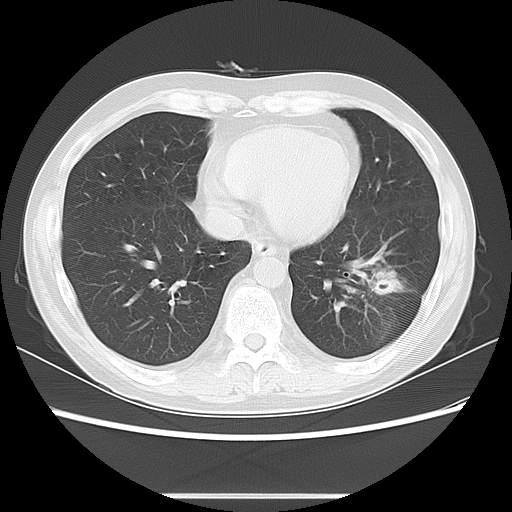
Chest CT, one axial slice. Position 26 of 63 along the scan axis. Reconstruction kernel LUNG. 120 kVp. Lung window (W 1500 / L -600 HU). 5 mm slice thickness. 512 × 512 image matrix. Male patient, age 49 years. From the clinical record (not read from this slice): clinical TNM (as recorded): T3 N0 M0; histopathological grade: G2-3.
Outlined on this slice (bounding box drawn by a radiologist):
- lung tumour (recorded histology: squamous cell carcinoma): bounding box (x1, y1, x2, y2) in pixels: (365, 257, 413, 307)